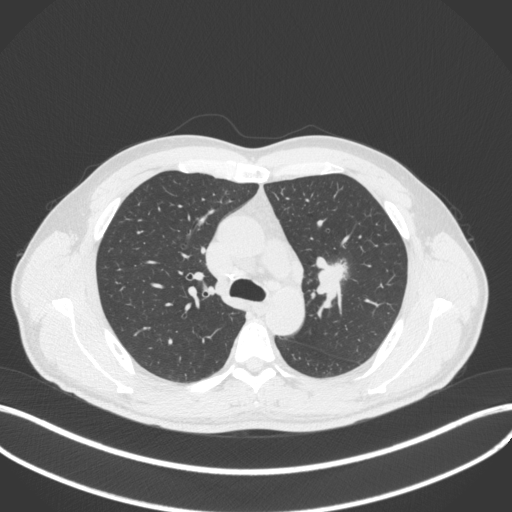
Chest CT, one axial slice. Position 286 of 383 along the scan axis. Lung window (W 1500 / L -600 HU). 1 mm slice thickness. 512 × 512 image matrix. Male patient, age 50 years. From the clinical record (not read from this slice): clinical TNM (as recorded): T1c N1 M1b.
Outlined on this slice (rectangle marked by the reading radiologist):
- lung tumour (recorded histology: squamous cell carcinoma): bounding box (x1, y1, x2, y2) in pixels: (311, 253, 350, 299)